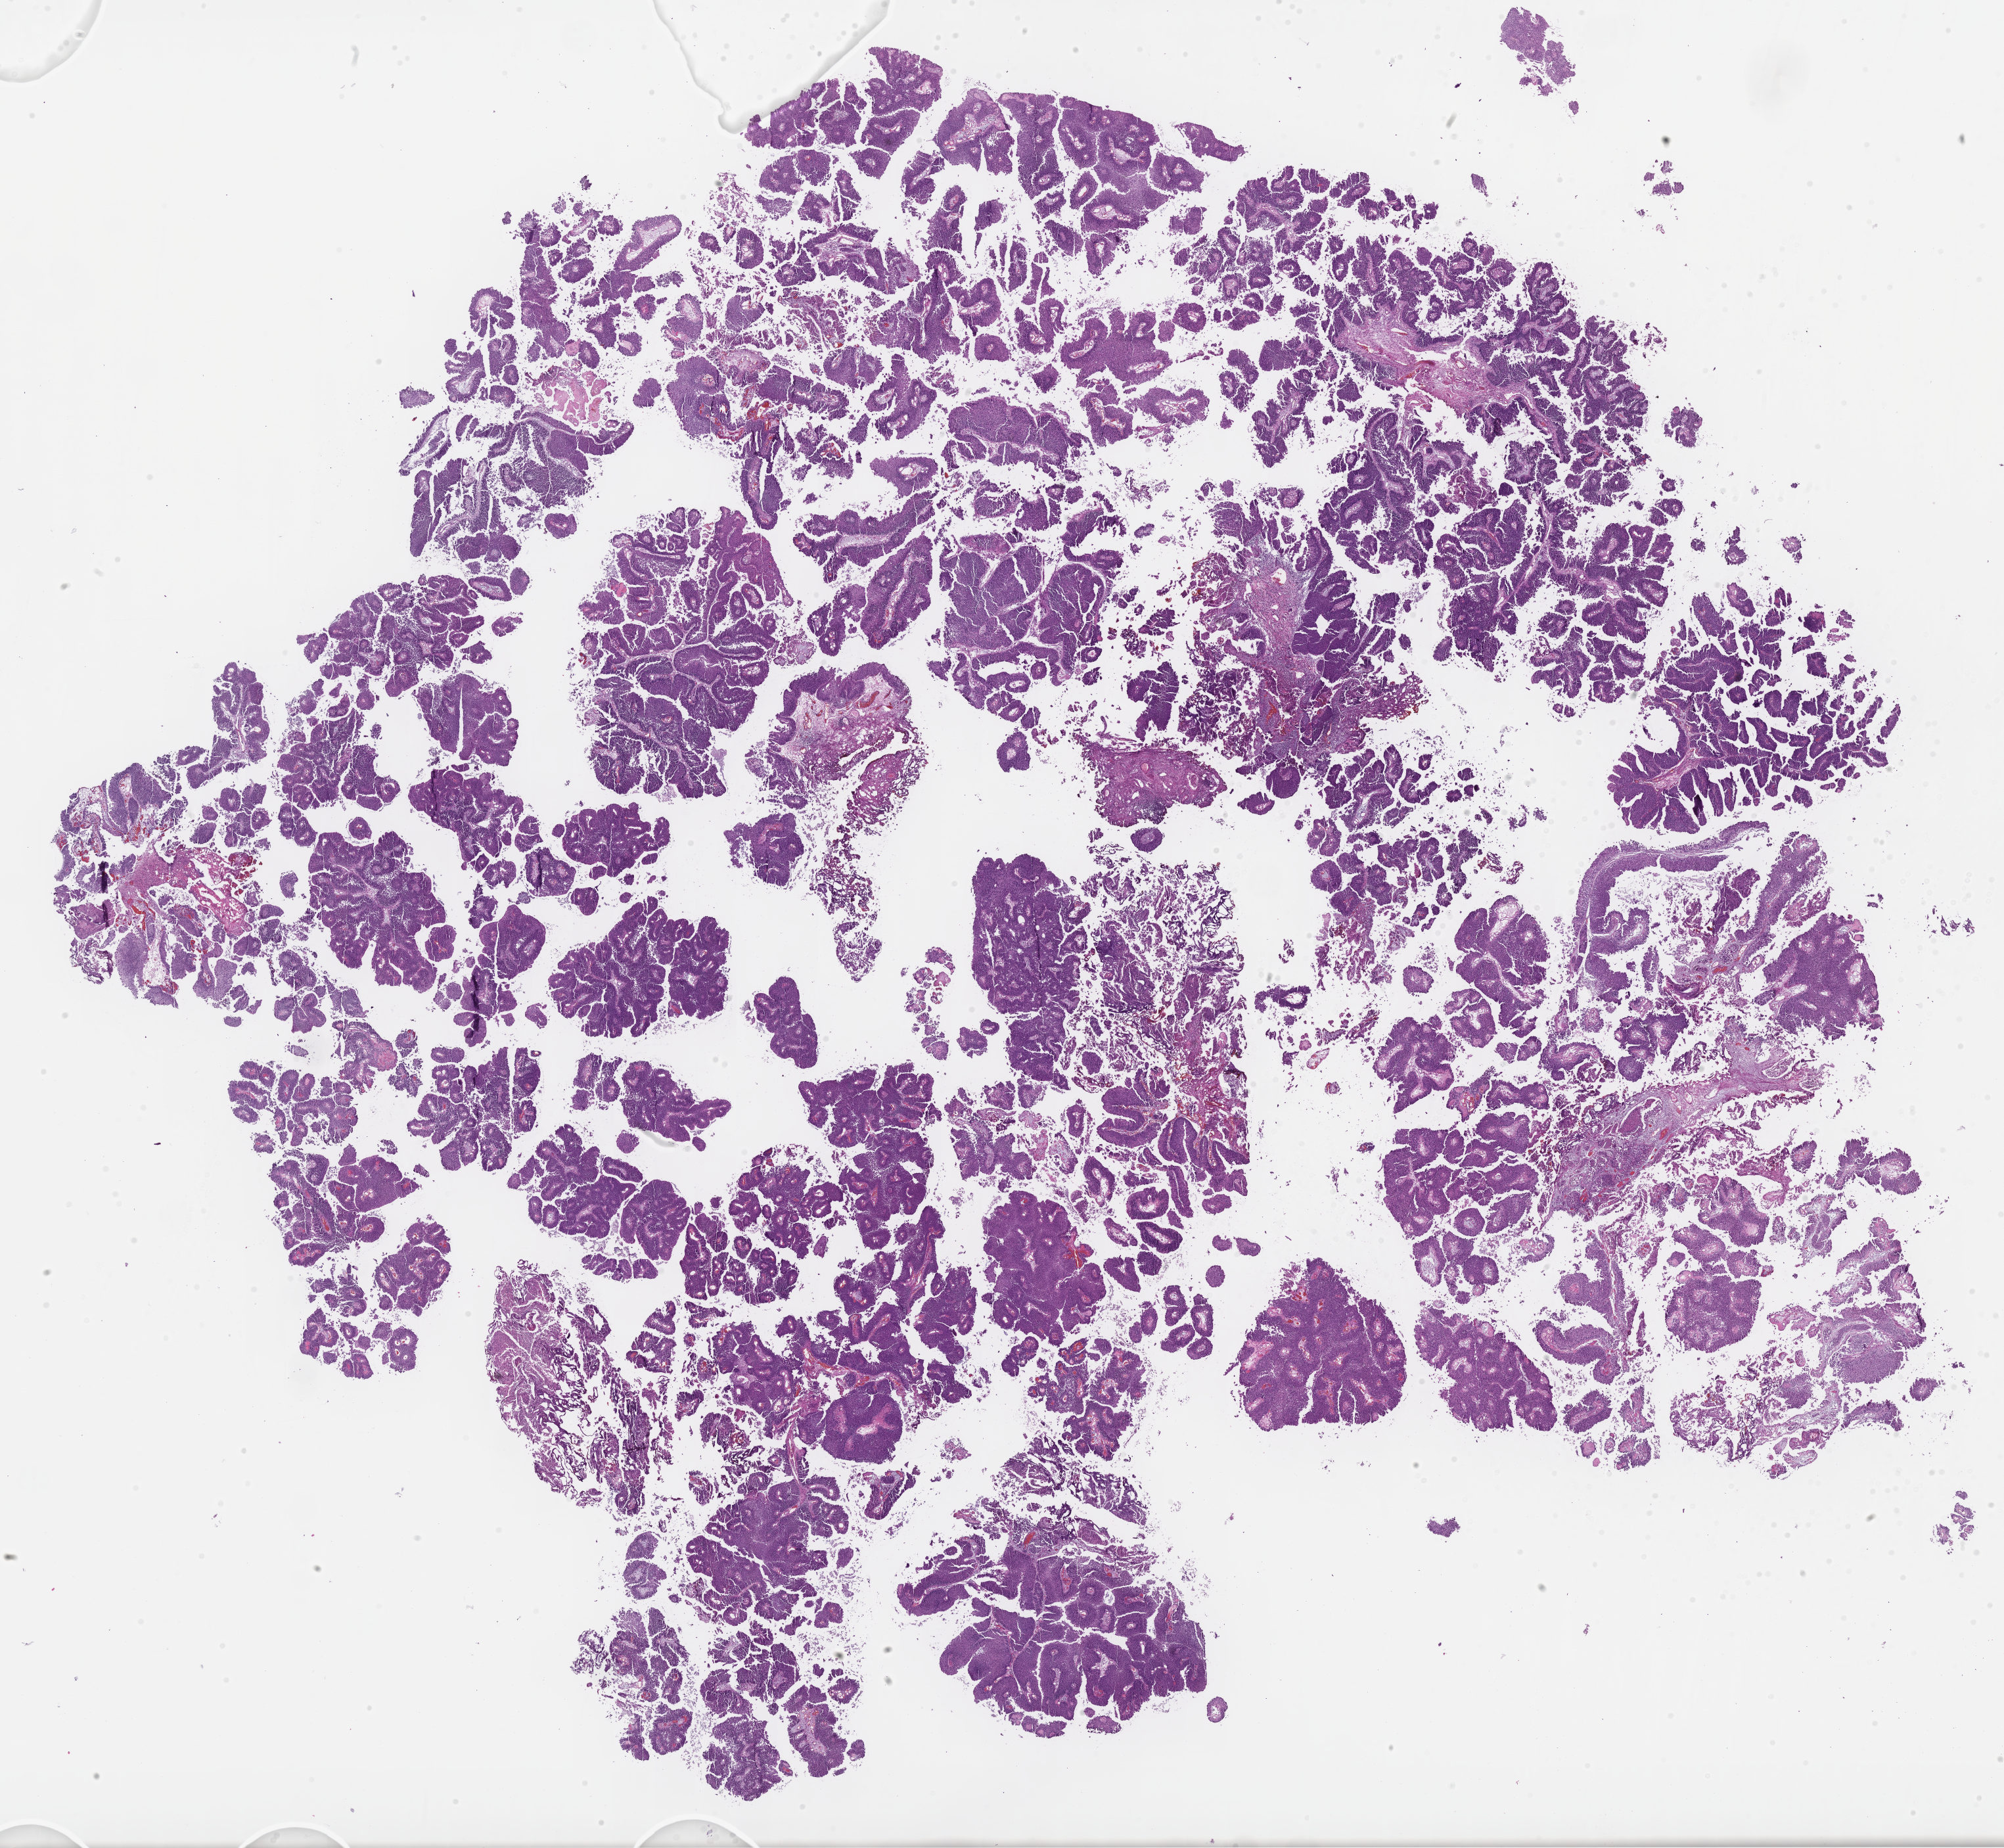
Digitized haematoxylin and eosin-stained section — low-resolution overview of the scanned area, about 24.6 x 22.7 mm. Formalin-fixed, paraffin-embedded (FFPE) tissue. Primary tumor. Site: lateral wall of bladder. Patient sex: female. Composition of this section per pathologist review: tumor cells 80%, tumor nuclei 95%, stromal cells 20%, necrosis 0%, normal cells 0%. Infiltration values recorded for this section: lymphocyte infiltration 0%, monocyte infiltration 0%, neutrophil infiltration 0%.
Section: top of the tissue portion. Histologic diagnosis: Papillary urothelial carcinoma.